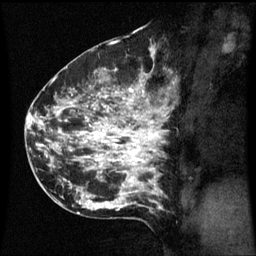
Breast MRI (dynamic contrast-enhanced), one sagittal slice; position 36 of 60 along the scan axis; dynamic contrast-enhanced series, image 2 of 3 at this slice position (ordered by acquisition); 1.5 T; TE 4.2 ms, TR 8.9 ms; 2.1 mm slice thickness; 256 × 256 image matrix, field of view 200 × 200 mm. Patient: female, 42 years. From the clinical record (not read from this slice): setting: breast cancer imaged before/during neoadjuvant chemotherapy; receptor status: HER2-positive.
Annotated regions visible in this slice (semi-automatic segmentation, software-assisted and operator-edited):
- analysis volume of interest (the breast-tissue region the enhancement analysis was run in; not a lesion): box from (x=66, y=82) to (x=171, y=193) px
- tumour enhancement mask (voxels above the 70 % enhancement threshold inside the analysis volume of interest): (x=80, y=84)–(x=167, y=187)